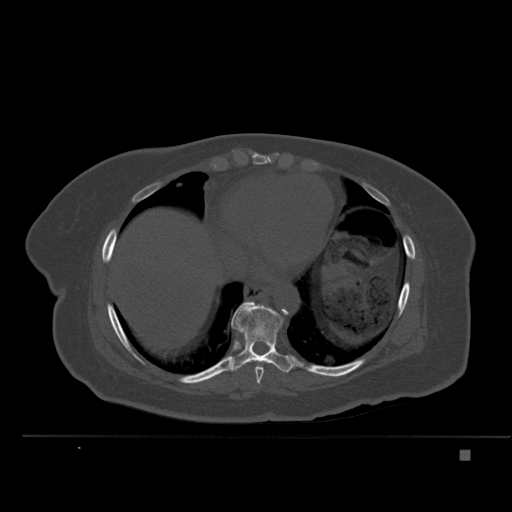
CT including the spine, one axial slice; position 300 of 477 along the scan axis; bone window (W 1800 / L 400 HU); 512 × 512 image matrix. Patient: female, 74 years. Case-level facts recorded for this patient, not image findings: primary cancer: colon.
Outlined on this slice (semi-automatically segmented with operator editing):
- T8 vertebra: bounding box (x1, y1, x2, y2) in pixels: (255, 366, 263, 384)
- T9 vertebra: (222, 301, 294, 373)